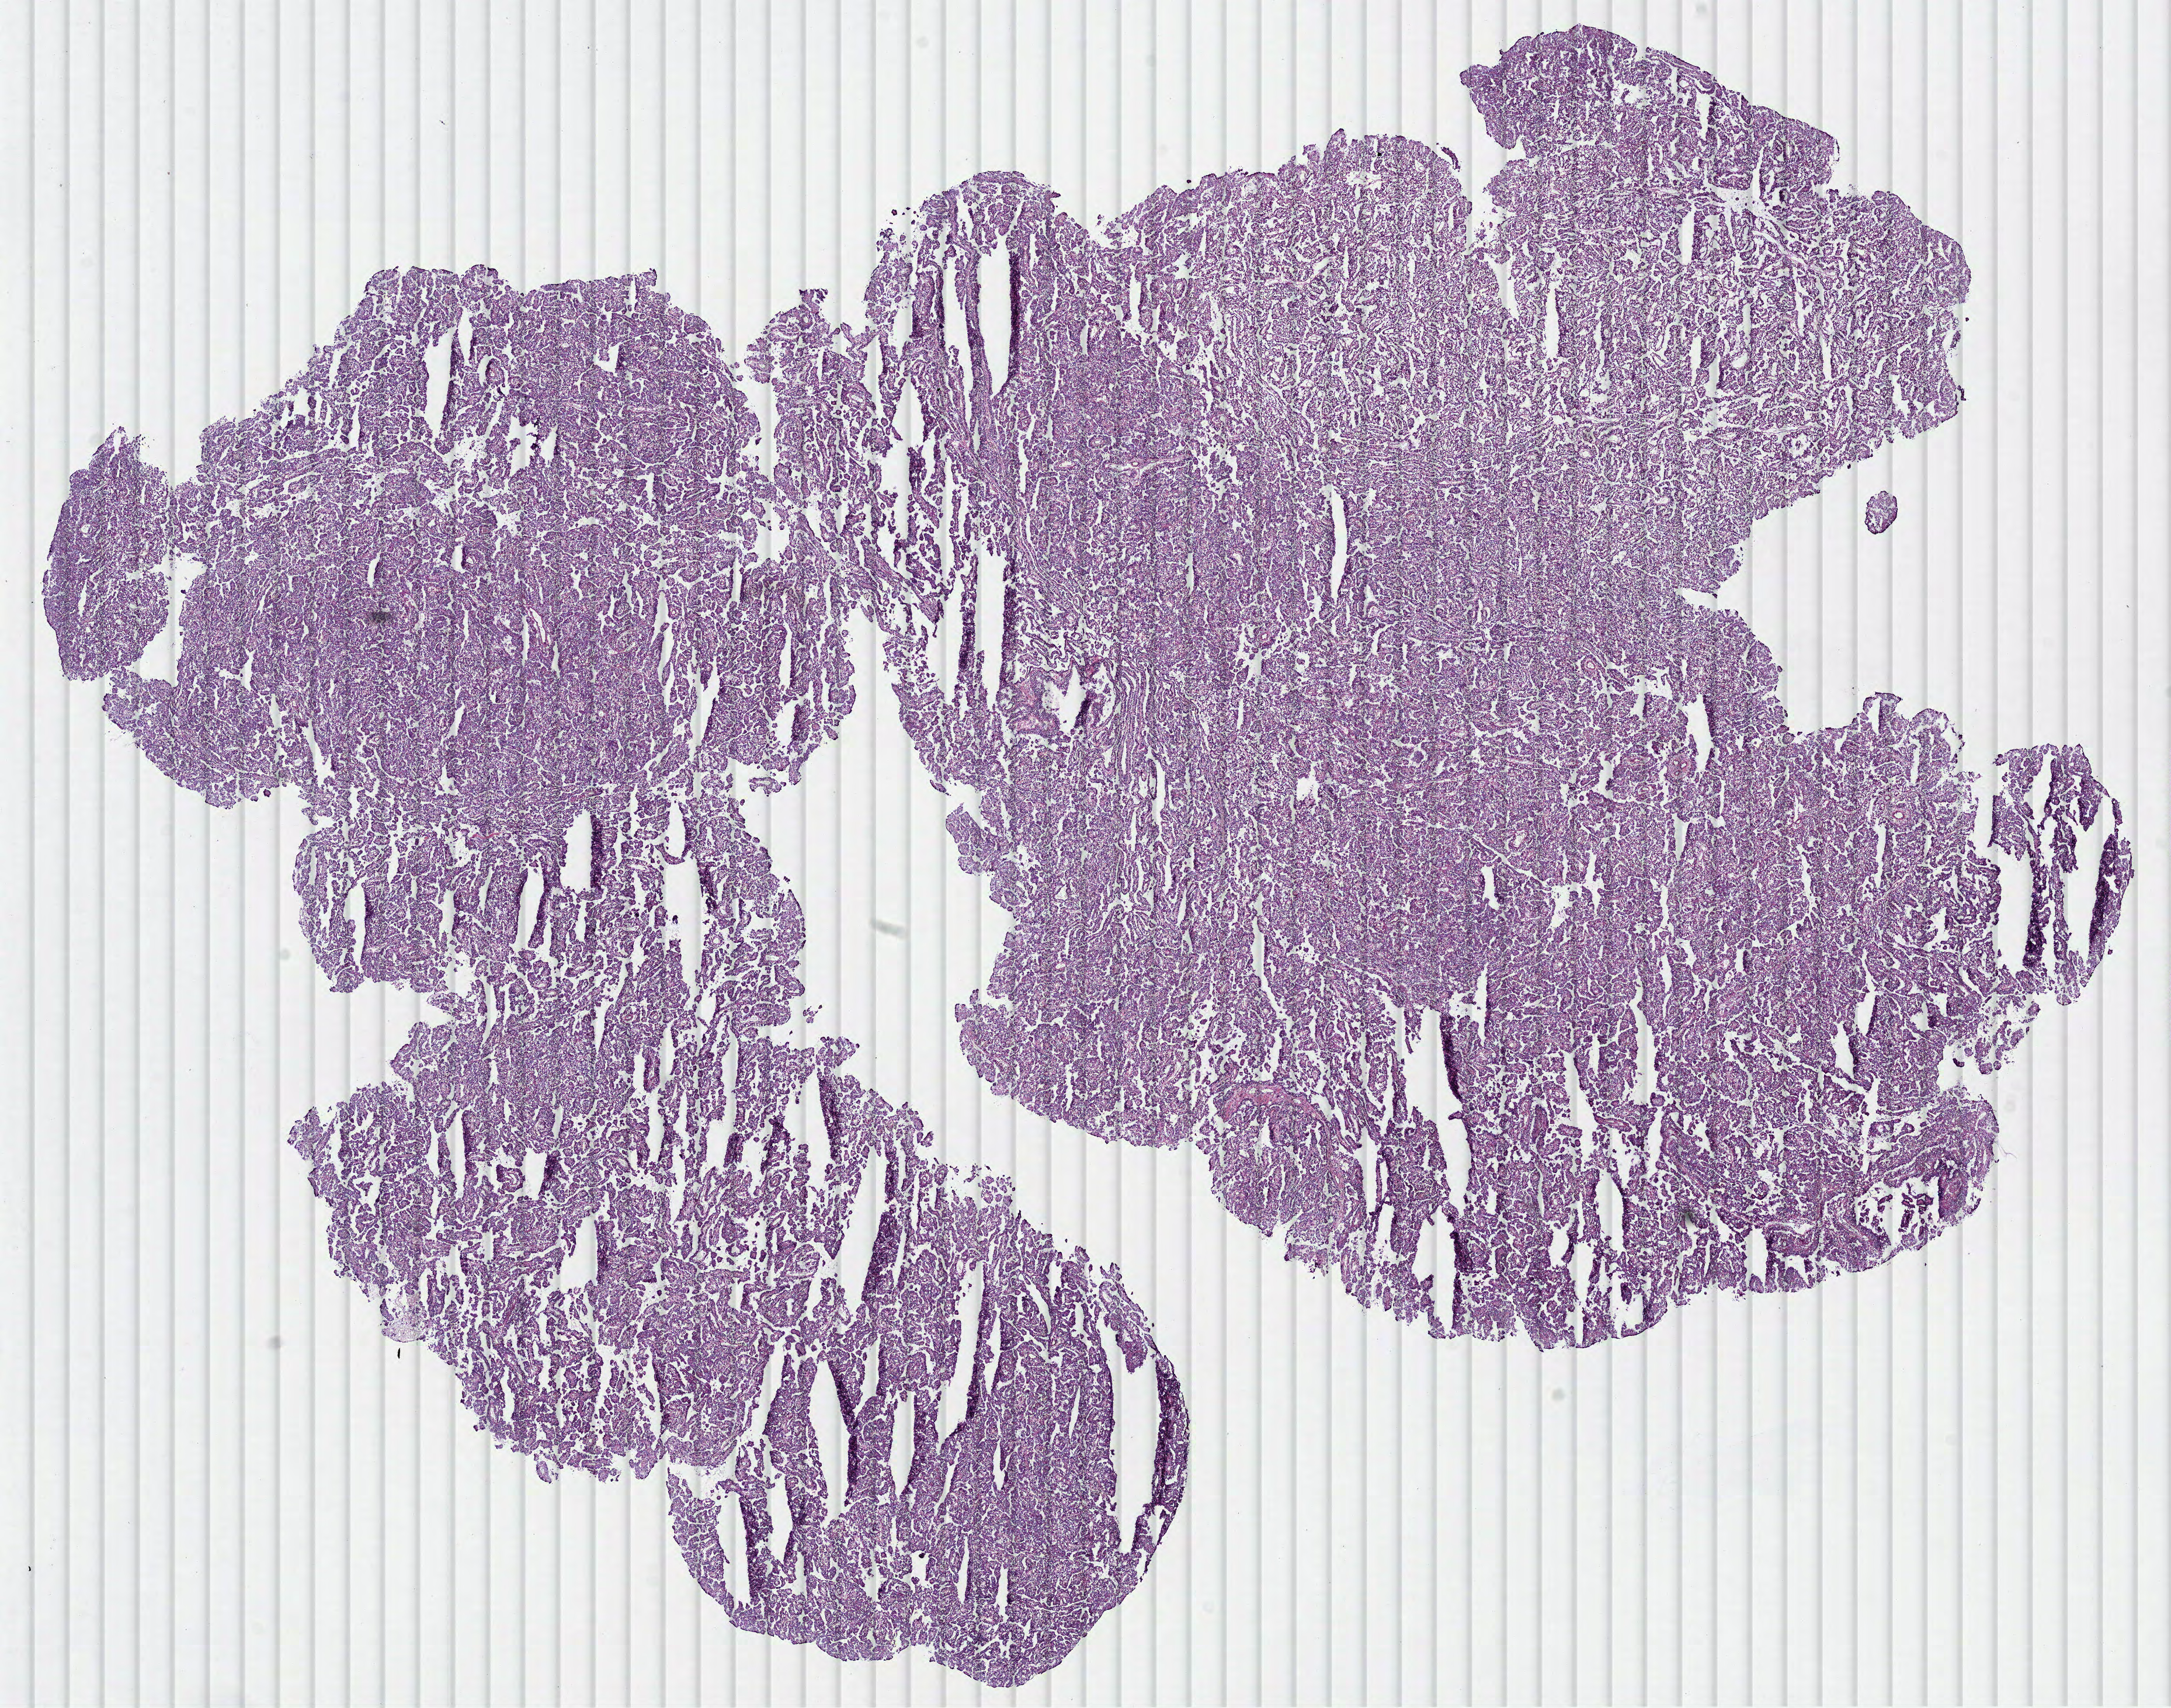
Digitized Hematoxylin and eosin (H&E) stained tissue section (whole slide) — shown as a low-resolution overview of the whole scanned area (about 15.0 x 11.8 mm, slide scanned at 40x); frozen section from the bottom of the tissue portion; primary tumour sample from the kidney. Patient: female, age at initial diagnosis 79 years.
Histologic diagnosis: Papillary adenocarcinoma, NOS.